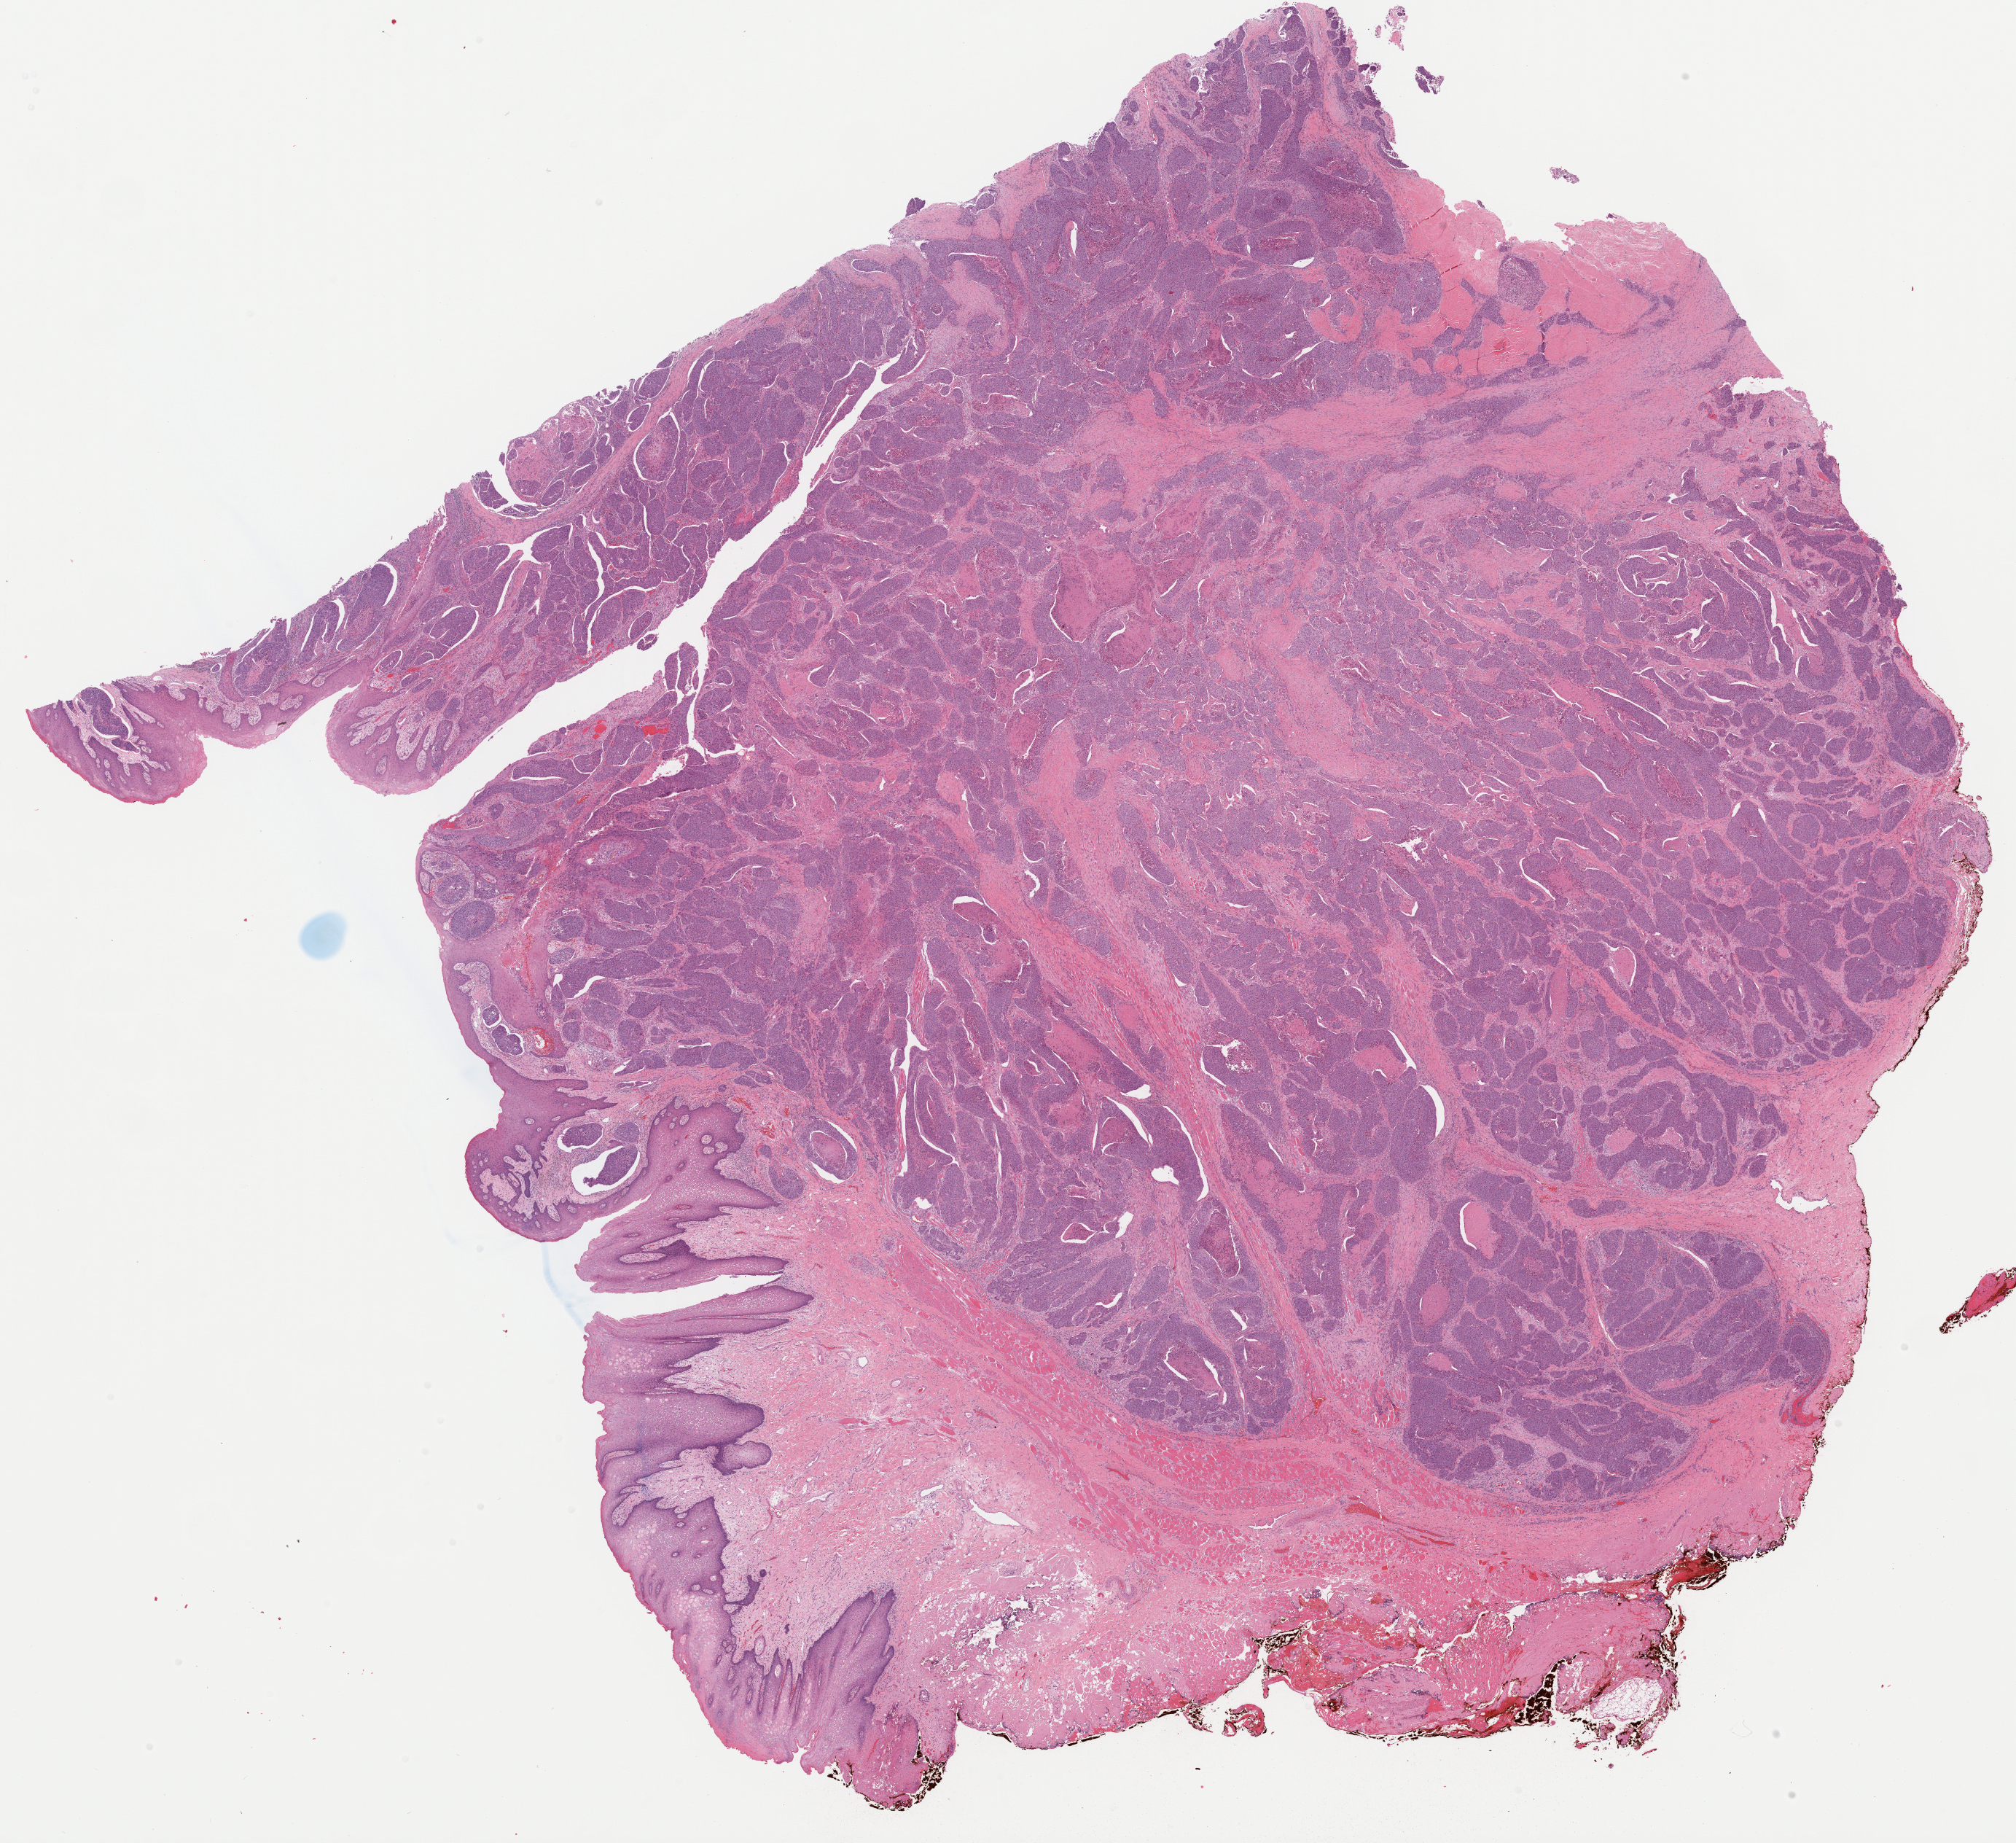
Whole-slide histology image, H&E-stained, low-resolution overview of the scanned area, about 21.8 x 19.9 mm, FFPE section, sample: primary tumour, head and neck. Male patient; age at initial diagnosis 49 years. Histologic grade: G2 (moderately differentiated).
TNM: T4 N2b MX. AJCC pathologic stage: IVA (6th edition). Diagnosis: Squamous cell carcinoma, NOS.